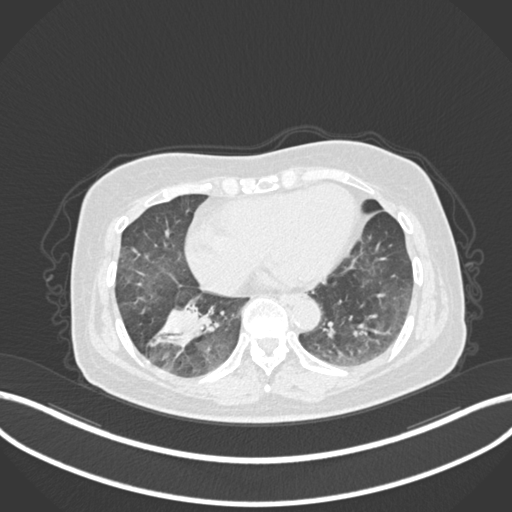
Chest CT, one axial slice; position 42 of 222 along the scan axis; reconstruction kernel B30f; 120 kVp; lung window (W 1500 / L -600 HU); 512 × 512 image matrix. Female patient, age 67 years. Case-level facts recorded for this patient, not image findings: clinical TNM (as recorded): T1c N1 M0.
Annotated regions visible in this slice (rectangle marked by the reading radiologist):
- lung tumour (recorded histology: adenocarcinoma): box from (x=145, y=299) to (x=221, y=357) px